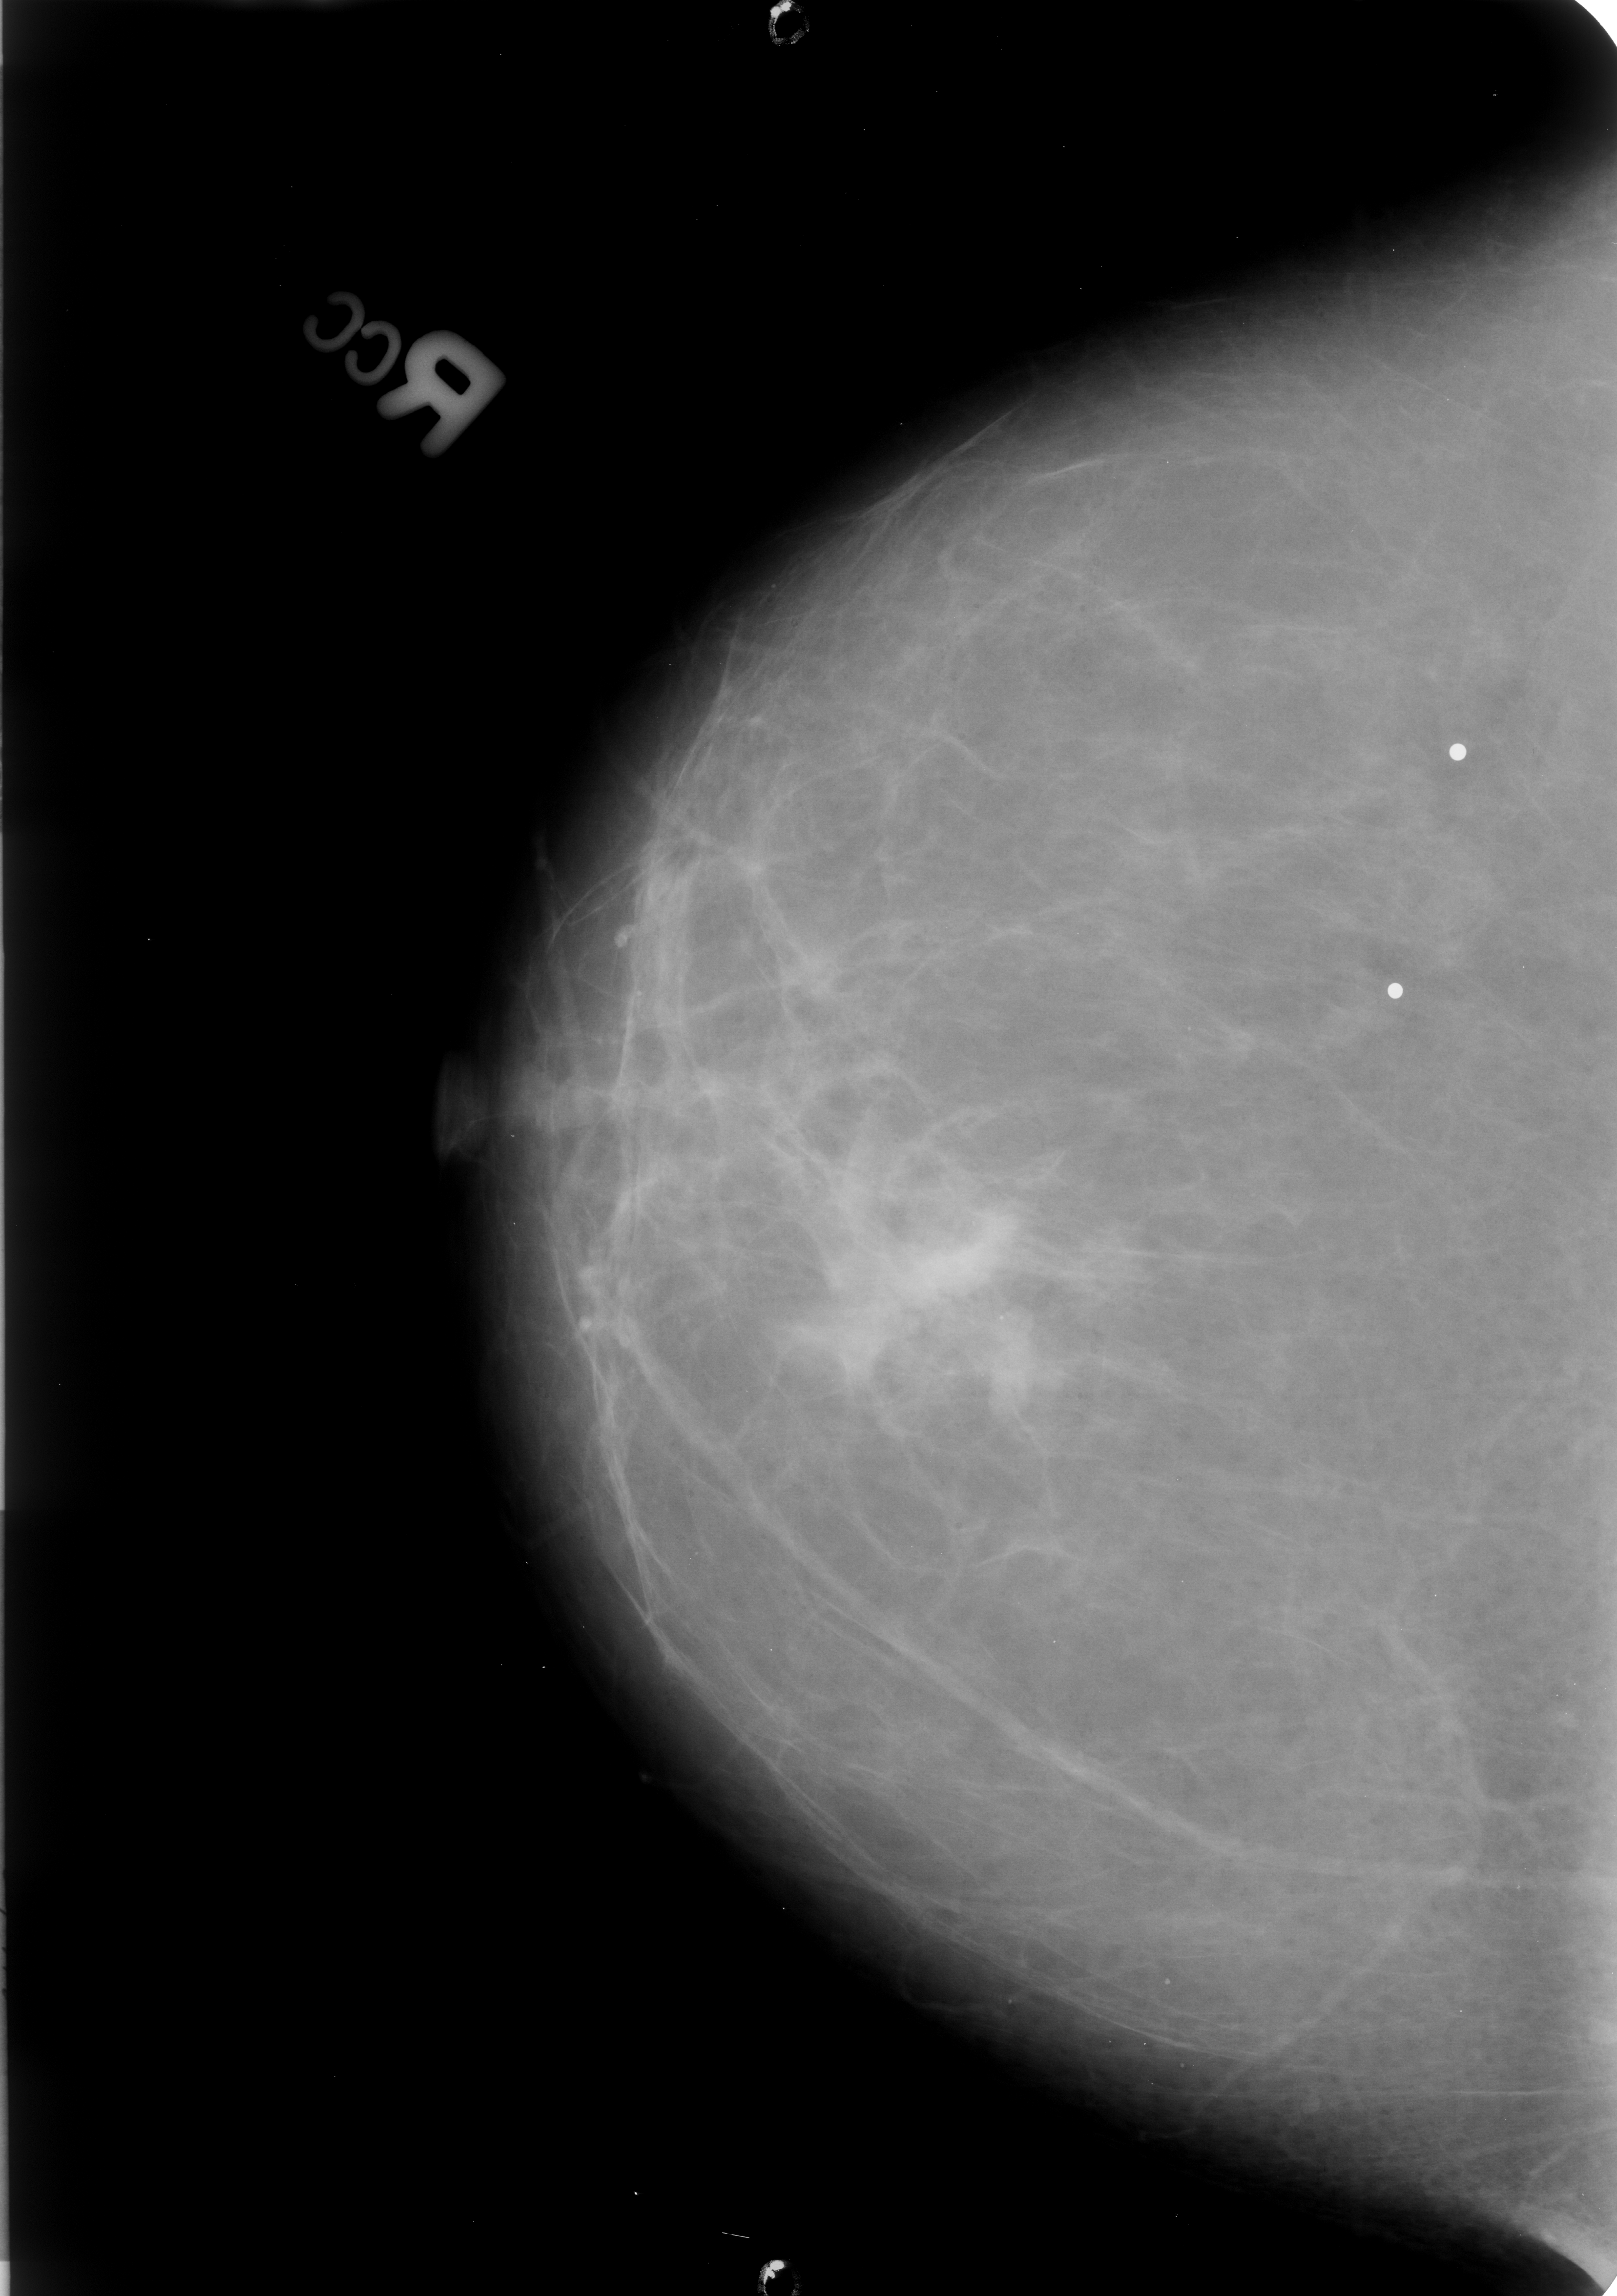
Digitized screen-film mammogram; right breast; CC view; BI-RADS breast density category 1 (scale 1–4); 1617 × 2296 image matrix.
Marked abnormalities (boxes around the expert regions of interest):
- mass, shape irregular / architectural distortion, margins ill defined / spiculated; BI-RADS assessment category 4; pathology result (as recorded, not read from the image): malignant: bounding box <807,1224,996,1390> (left, top, right, bottom; pixels)